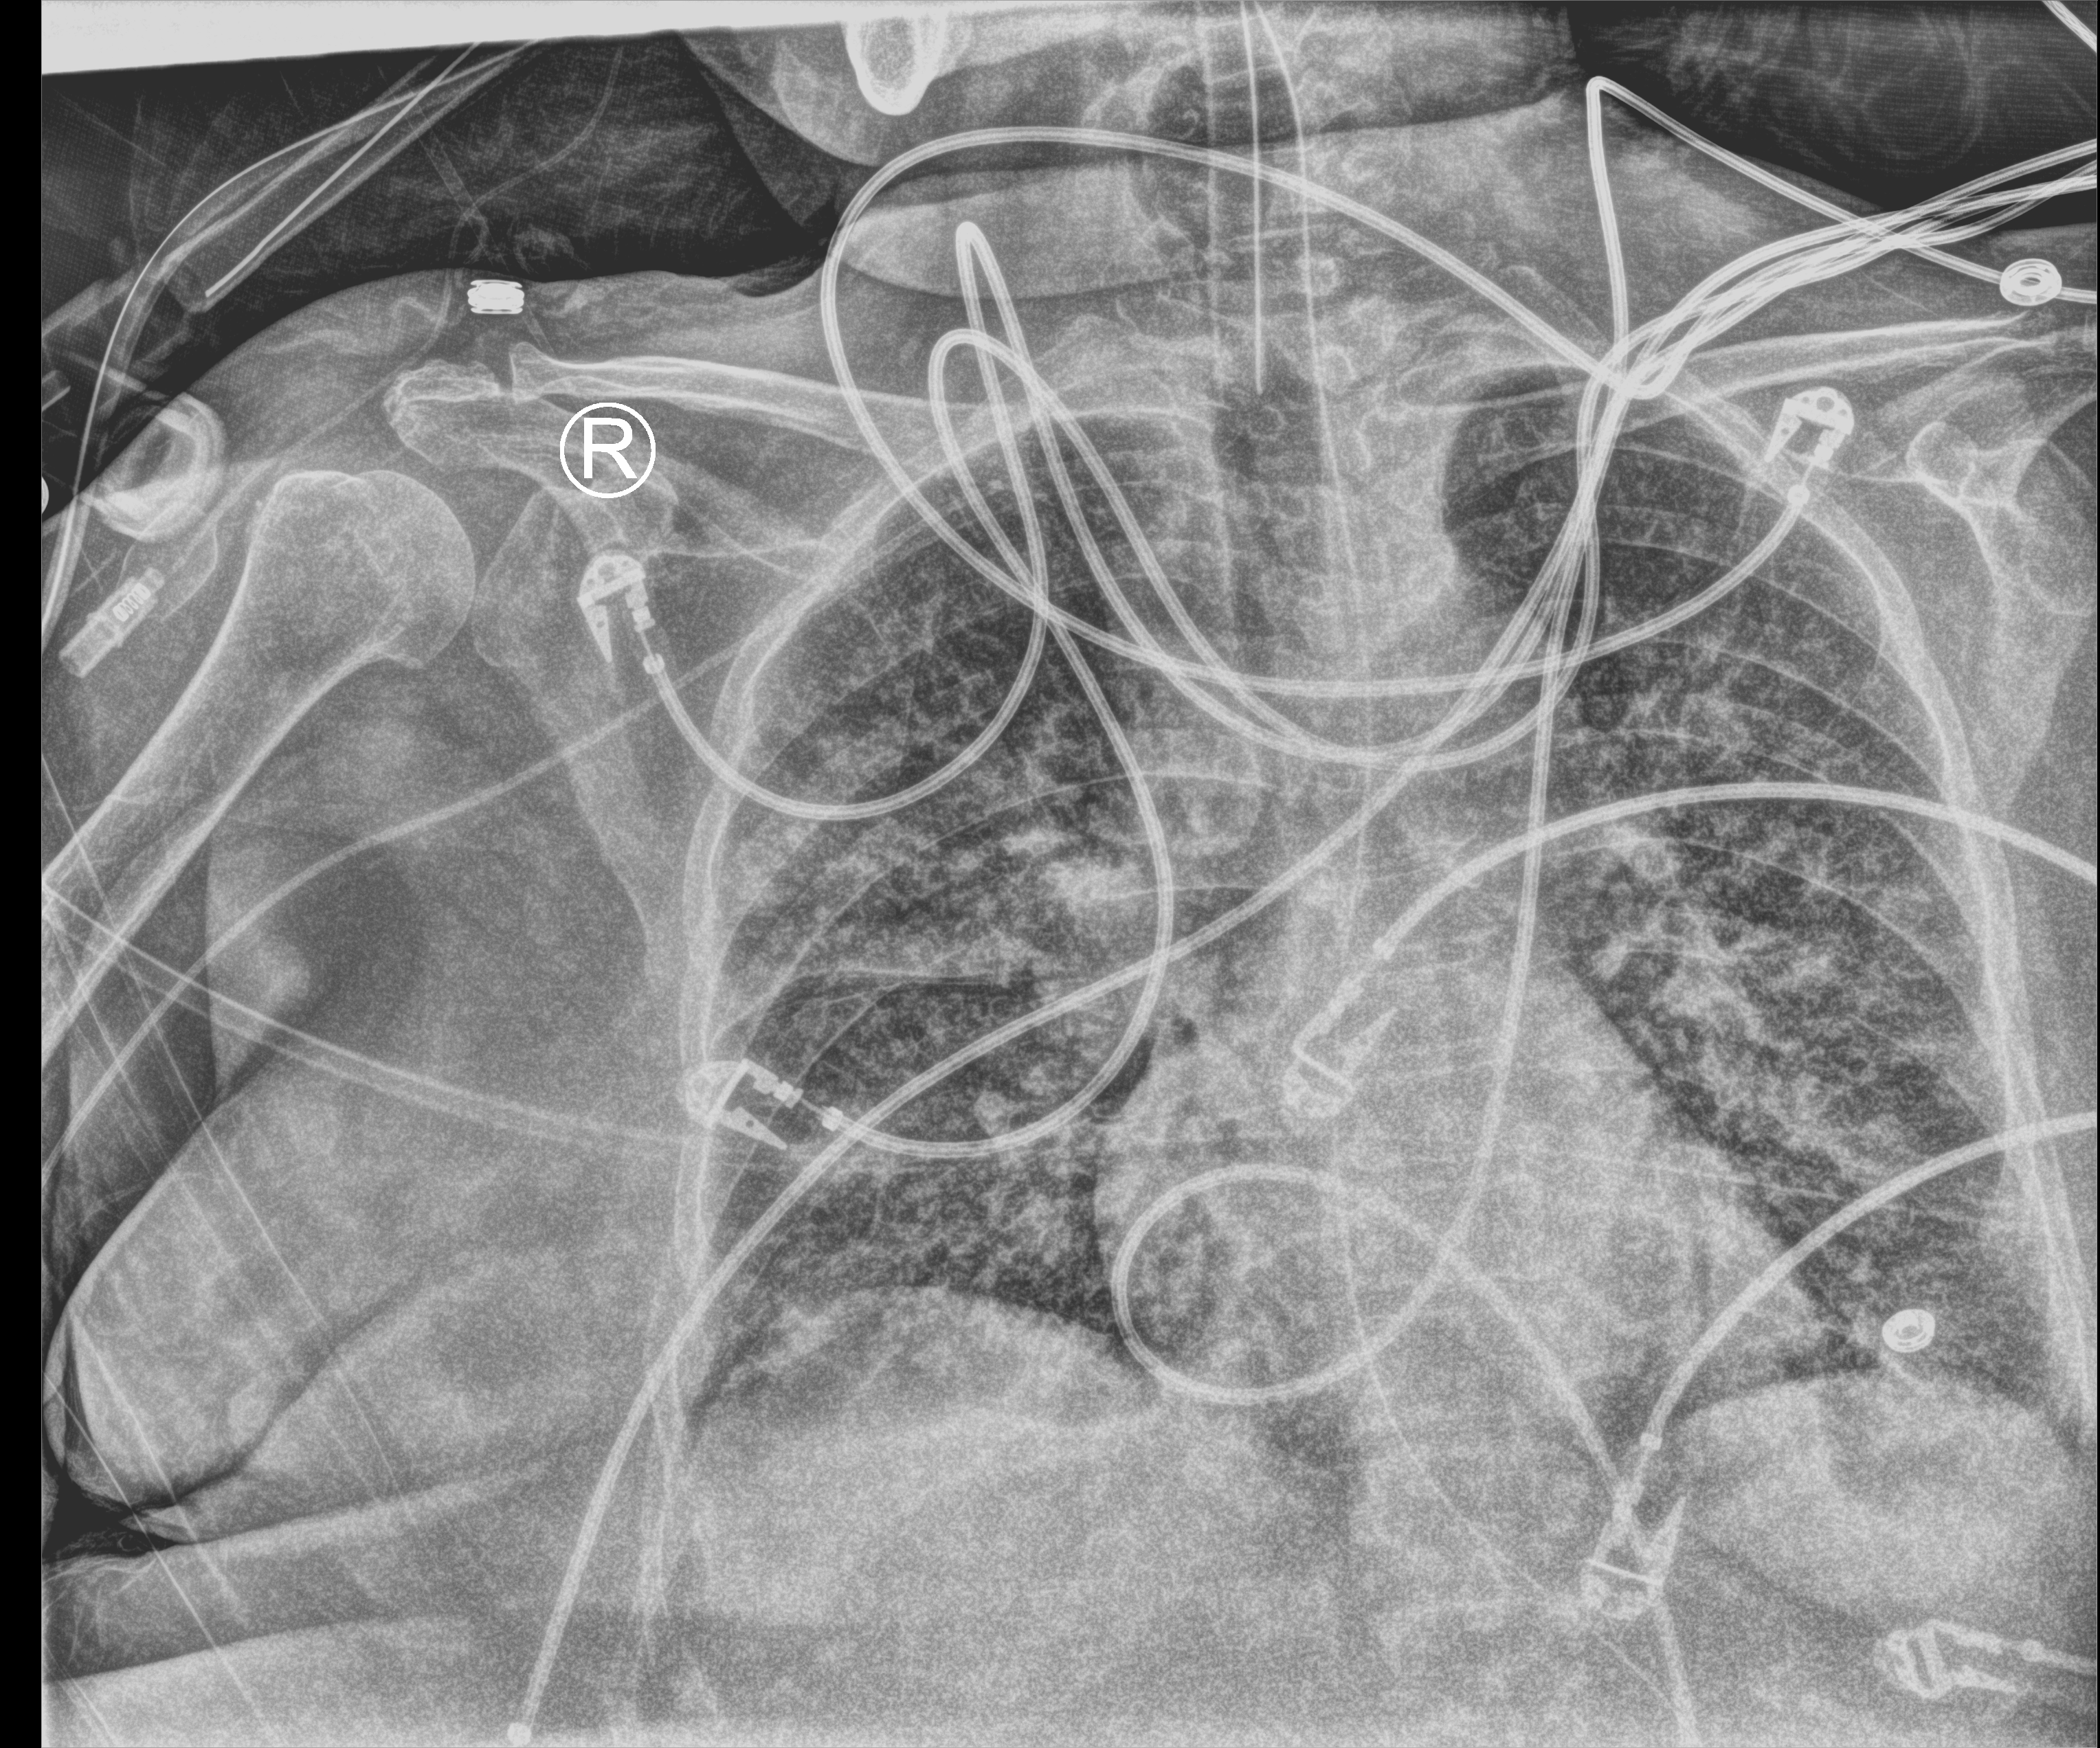
Portable chest radiograph, anteroposterior (AP) projection. Female patient hospitalised with COVID-19, age 60–74 years.
From the hospital-stay record, not from the radiograph (when in the stay this image was taken is not recorded): admitted to intensive care during this hospital stay: yes; length of hospital stay: 15 days; mechanically ventilated during this hospital stay: yes.